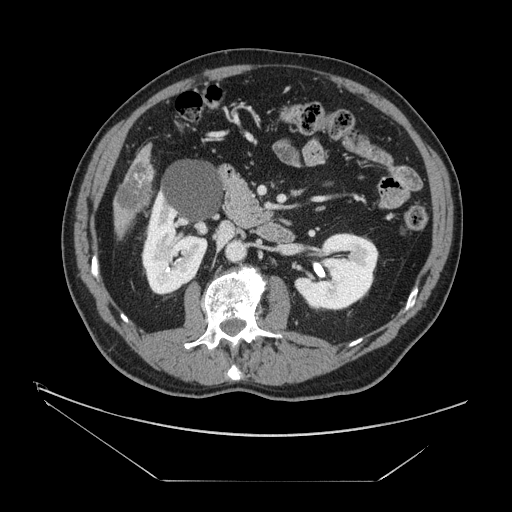
Contrast-enhanced abdominal CT, one axial slice. Position 53 of 161 along the scan axis. Reconstruction kernel STANDARD. 120 kVp. Intravenous contrast given. Soft-tissue window (W 400 / L 40 HU). 2.5 mm slice thickness. 512 × 512 image matrix. Male patient, age 65 years. Case-level facts recorded for this patient, not image findings: diagnosis: colorectal cancer liver metastases, imaged before liver resection; multiple liver metastases: yes; largest metastasis: 4.2 cm; disease in both lobes: yes.
Outlined on this slice (outlined manually by an expert reader):
- liver: bounding box [x1, y1, x2, y2] px = [116, 150, 153, 227]
- liver metastasis: [118, 166, 152, 210]